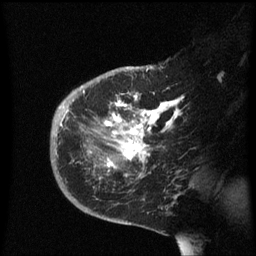
Breast MRI (dynamic contrast-enhanced), one sagittal slice; slice 39 of 60 in the series (ordered by position); dynamic contrast-enhanced series, image 2 of 3 at this slice position (ordered by acquisition); 1.5 T; TE 4.2 ms, TR 8.4 ms; 2.3 mm slice thickness; 256 × 256 image matrix, field of view 200 × 200 mm. Patient: female, 38 years. Case-level facts recorded for this patient, not image findings: setting: breast cancer imaged before/during neoadjuvant chemotherapy; receptor status: HER2-positive.
Structures marked on this image (semi-automatic segmentation, software-assisted and operator-edited):
- analysis volume of interest (the breast-tissue region the enhancement analysis was run in; not a lesion): box from (x=50, y=78) to (x=191, y=213) px
- tumour enhancement mask (voxels above the 70 % enhancement threshold inside the analysis volume of interest): (x=60, y=92)–(x=179, y=177)